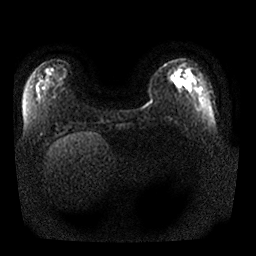
Breast MRI, one axial slice. Slice 6 of 25 in the series (ordered by position). Diffusion-weighted series; image 2 of 4 stored at this slice position (different b-values; order by instance number). 1.5 T. 4 mm slice thickness. 256 × 256 image matrix, field of view 350 × 350 mm. Female patient.
Outlined on this slice (manually delineated by an expert):
- tumour on diffusion-weighted imaging: bounding box <173,66,182,84> (left, top, right, bottom; pixels)